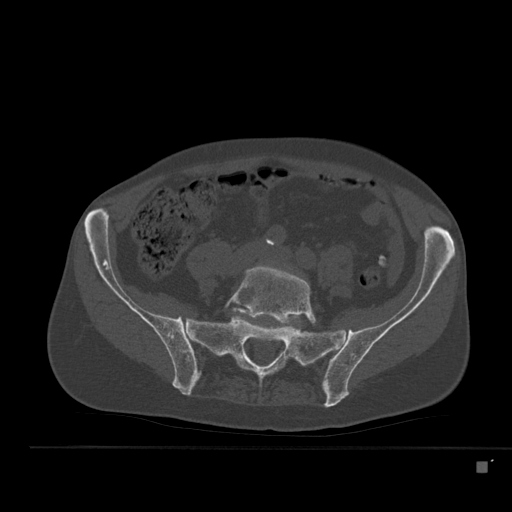
CT including the spine, one axial slice. Bone window (W 1800 / L 400 HU). 1.5 mm slice thickness. 512 × 512 image matrix, field of view 408 × 408 mm. Patient: male, 70 years. From the clinical record (not read from this slice): primary cancer: renal; vertebrae with lytic lesions (as recorded): T4, T6, T10, T12, L3, L4, L5.
Annotated regions visible in this slice (semi-automatically segmented with operator editing):
- L5 vertebra: bounding box (x1, y1, x2, y2) in pixels: (224, 266, 317, 324)